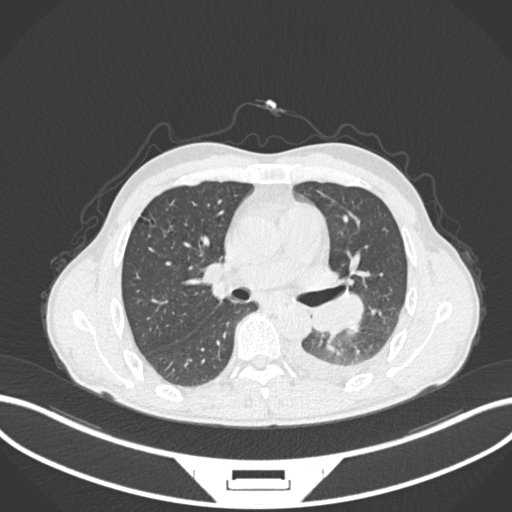
Chest CT, one axial slice. Slice 142 of 222 in the series (ordered by position). Reconstruction kernel B30f. 120 kVp. Lung window (W 1500 / L -600 HU). 1 mm slice thickness. 512 × 512 image matrix, field of view 400 × 400 mm. Male patient, age 47 years. Case-level facts recorded for this patient, not image findings: clinical TNM (as recorded): T3 N1 M1c.
Annotated regions visible in this slice (rectangle marked by the reading radiologist):
- lung tumour (recorded histology: small cell carcinoma): bounding box (x1, y1, x2, y2) in pixels: (311, 290, 364, 338)